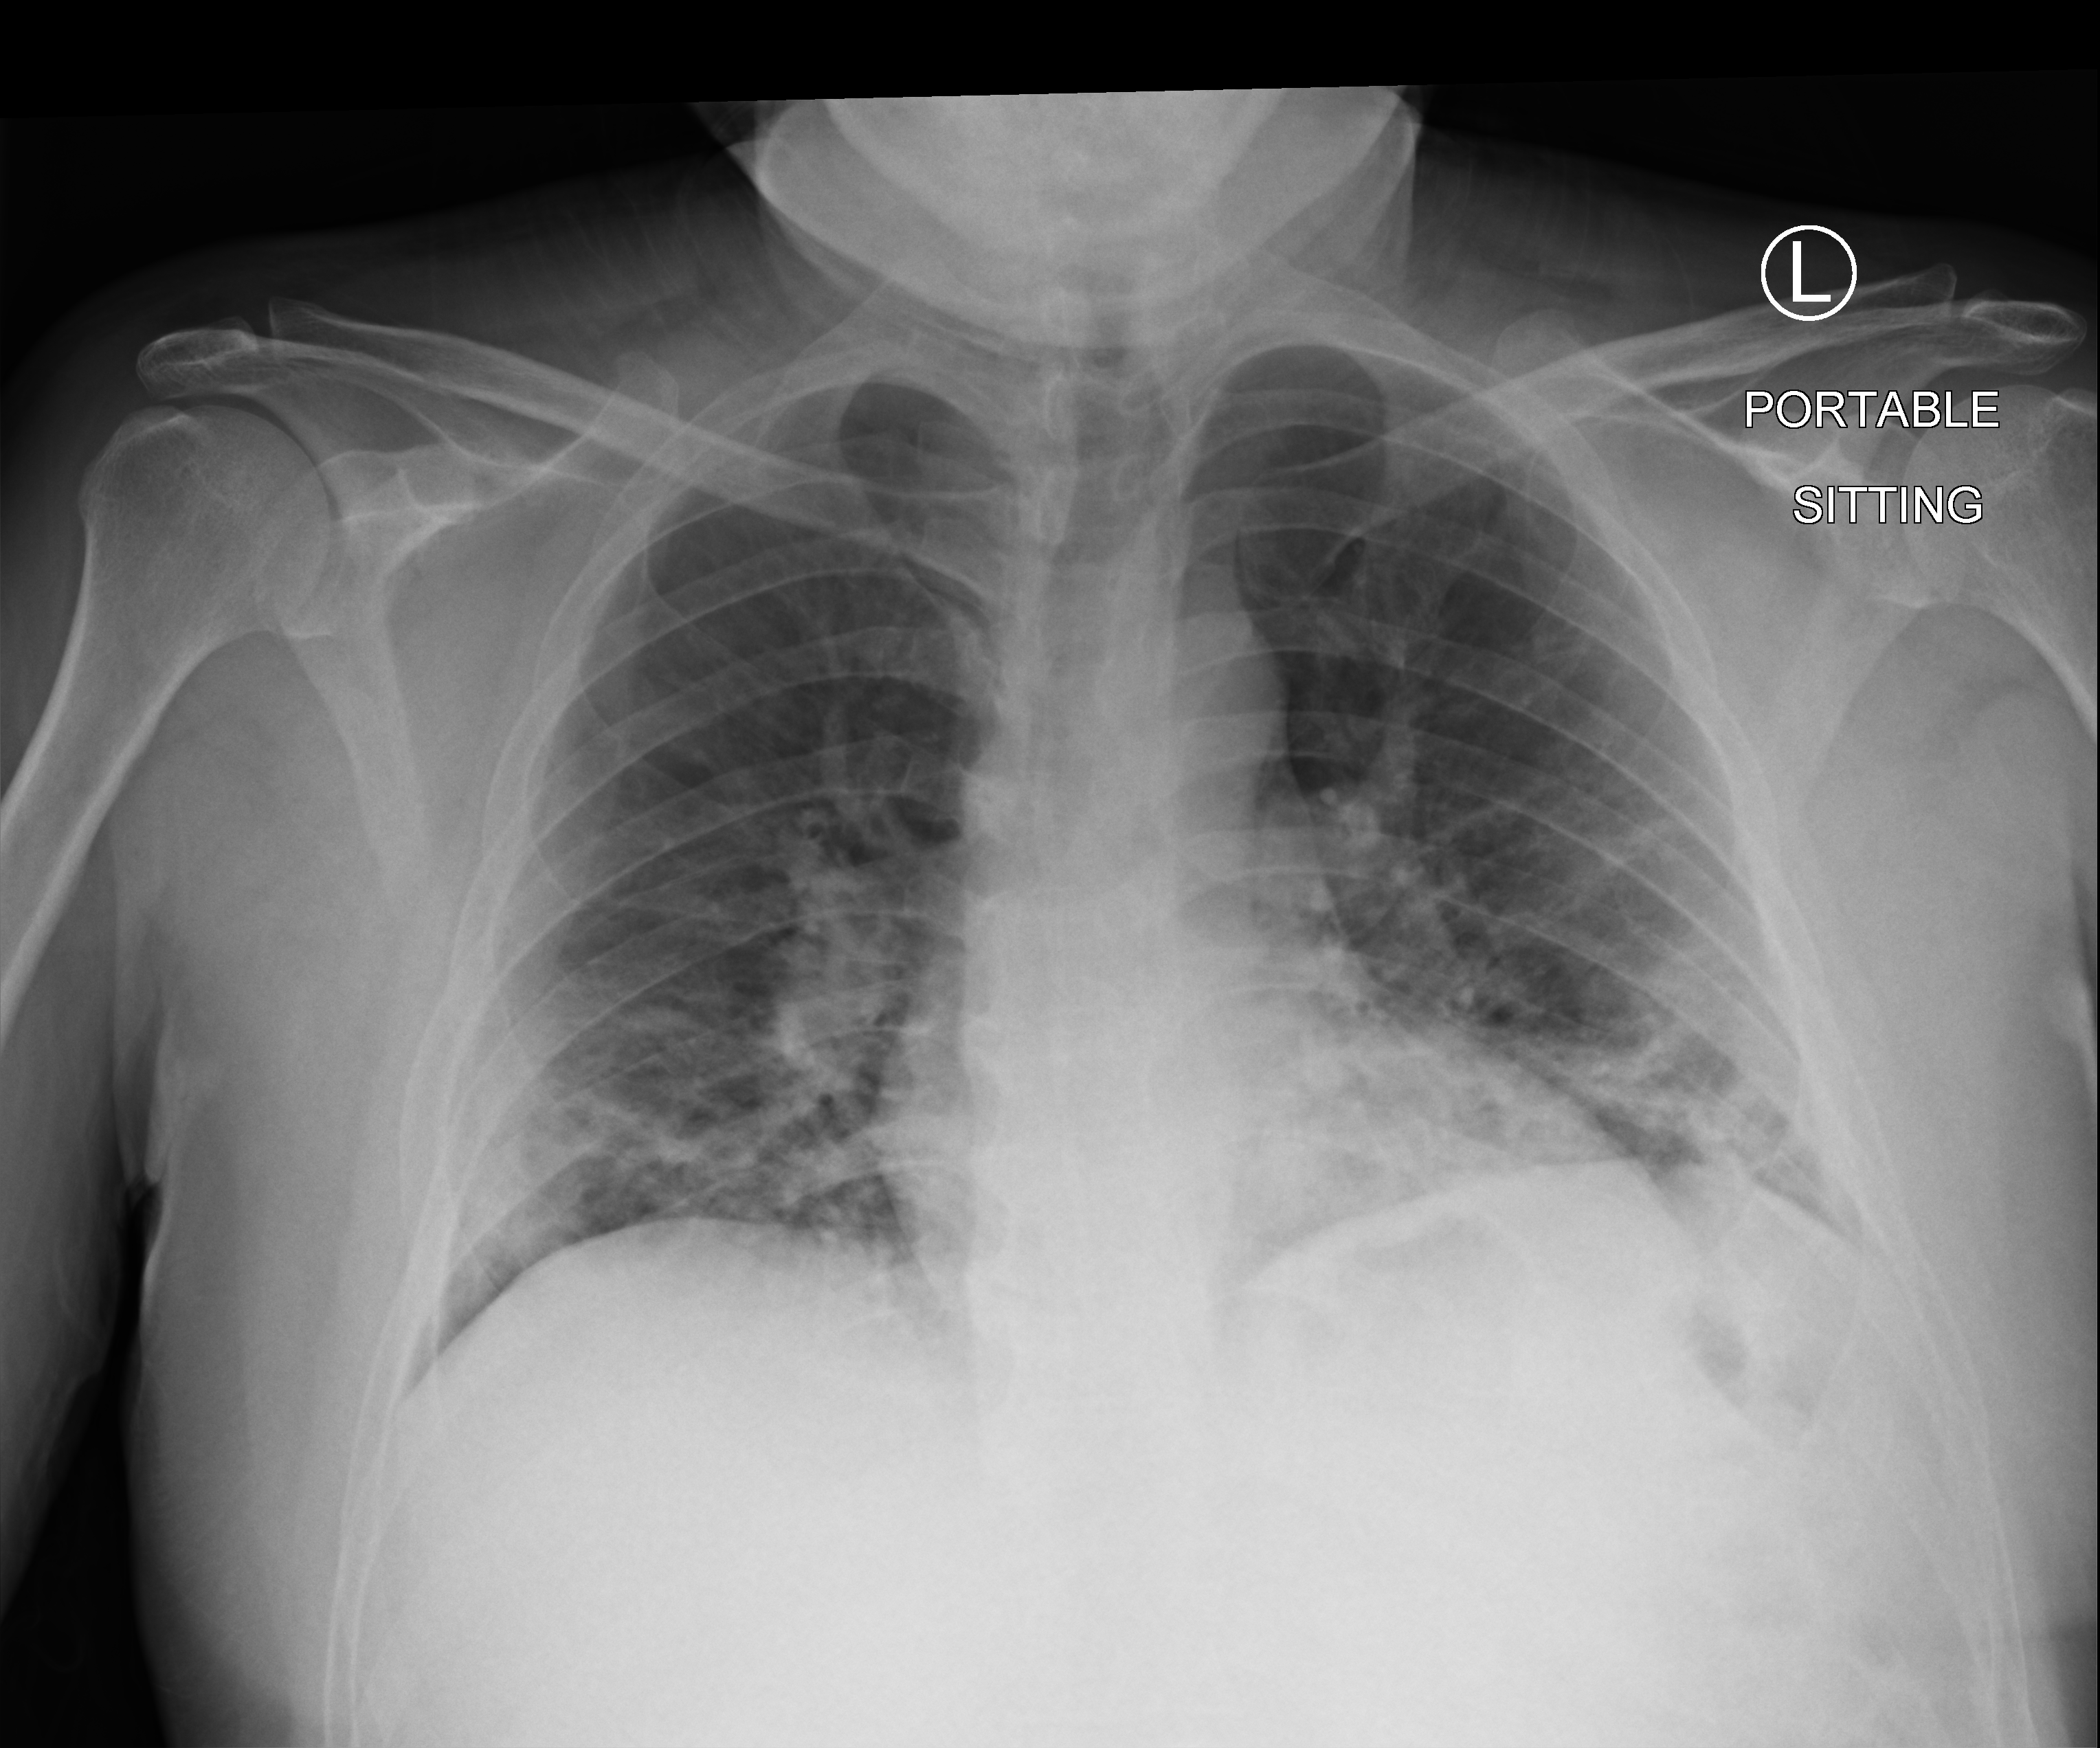
Bedside chest radiograph (computed radiography); anteroposterior (AP) projection. Patient hospitalised with COVID-19; male, aged 18–59 years.
From the hospital-stay record, not from the radiograph (when in the stay this image was taken is not recorded):
- smoking status (admission record): never